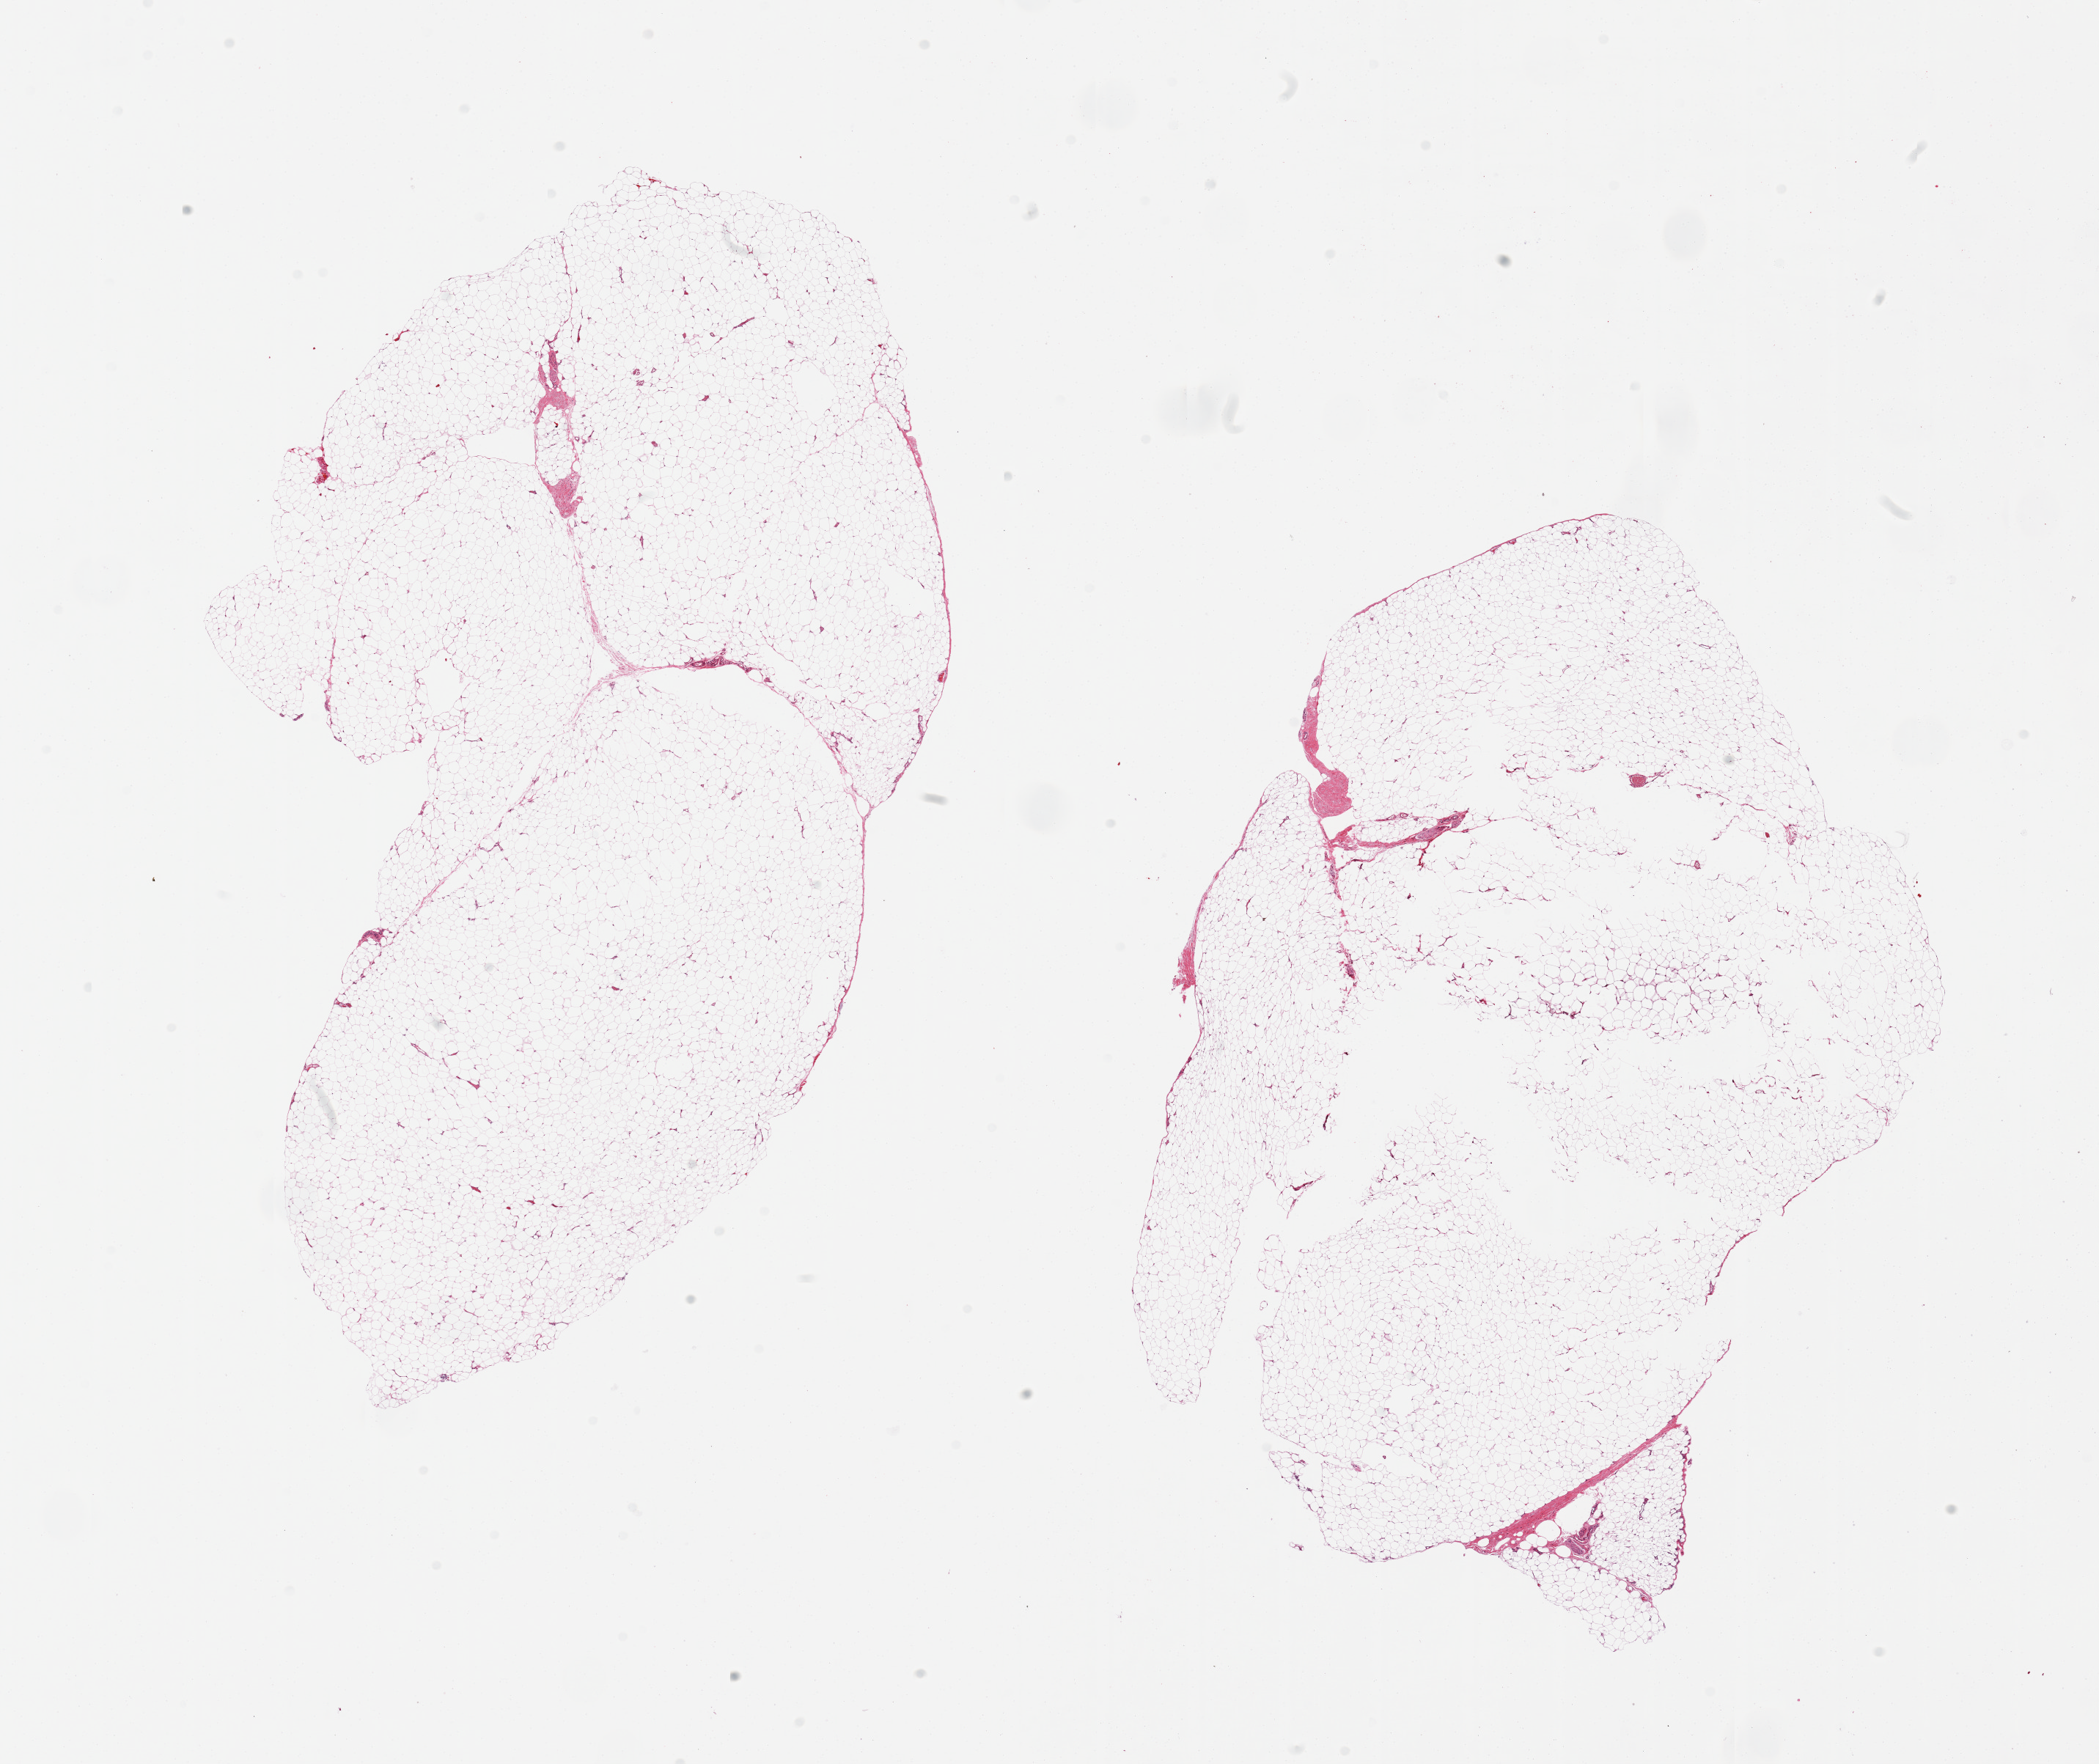
Digitized H&E-stained section, brightfield — whole scanned area (about 22.6 x 19.0 mm) shown as a low-resolution overview; PAXgene-fixed paraffin-embedded (PFPE) section; section of adipose tissue (target tissue); donor tissue sample.
Review note (as recorded): 2 pieces.